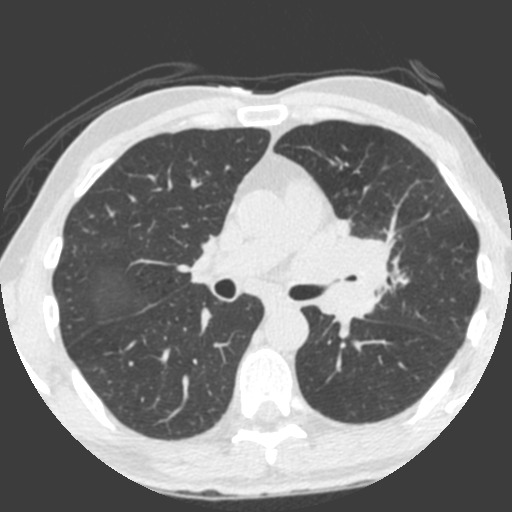
Axial slice from a low-dose chest CT screening exam, third annual screen, lung window (W 1500 / L -600 HU), slice 131 of 212 in the series. Male, age 55 years at enrolment. Current smoker at enrolment.
- Expert reader's lesion annotation, bounding box (x1, y1, x2, y2) in pixels: (309, 214, 400, 325).
- The exam's reader record, not a measurement of the box and not confirmed to be the same lesion: non-calcified nodule or mass ≥4 mm, left upper lobe, 49 × 29 mm, spiculated (stellate) margins, soft tissue attenuation, pre-existing on the prior screen: yes; interval growth: yes.
- Participant outcome: lung cancer diagnosed 0 days after this screen — small cell carcinoma, NOS, left upper lobe, undifferentiated (G4), stage IV (AJCC 6th edition), 60 mm at pathology.